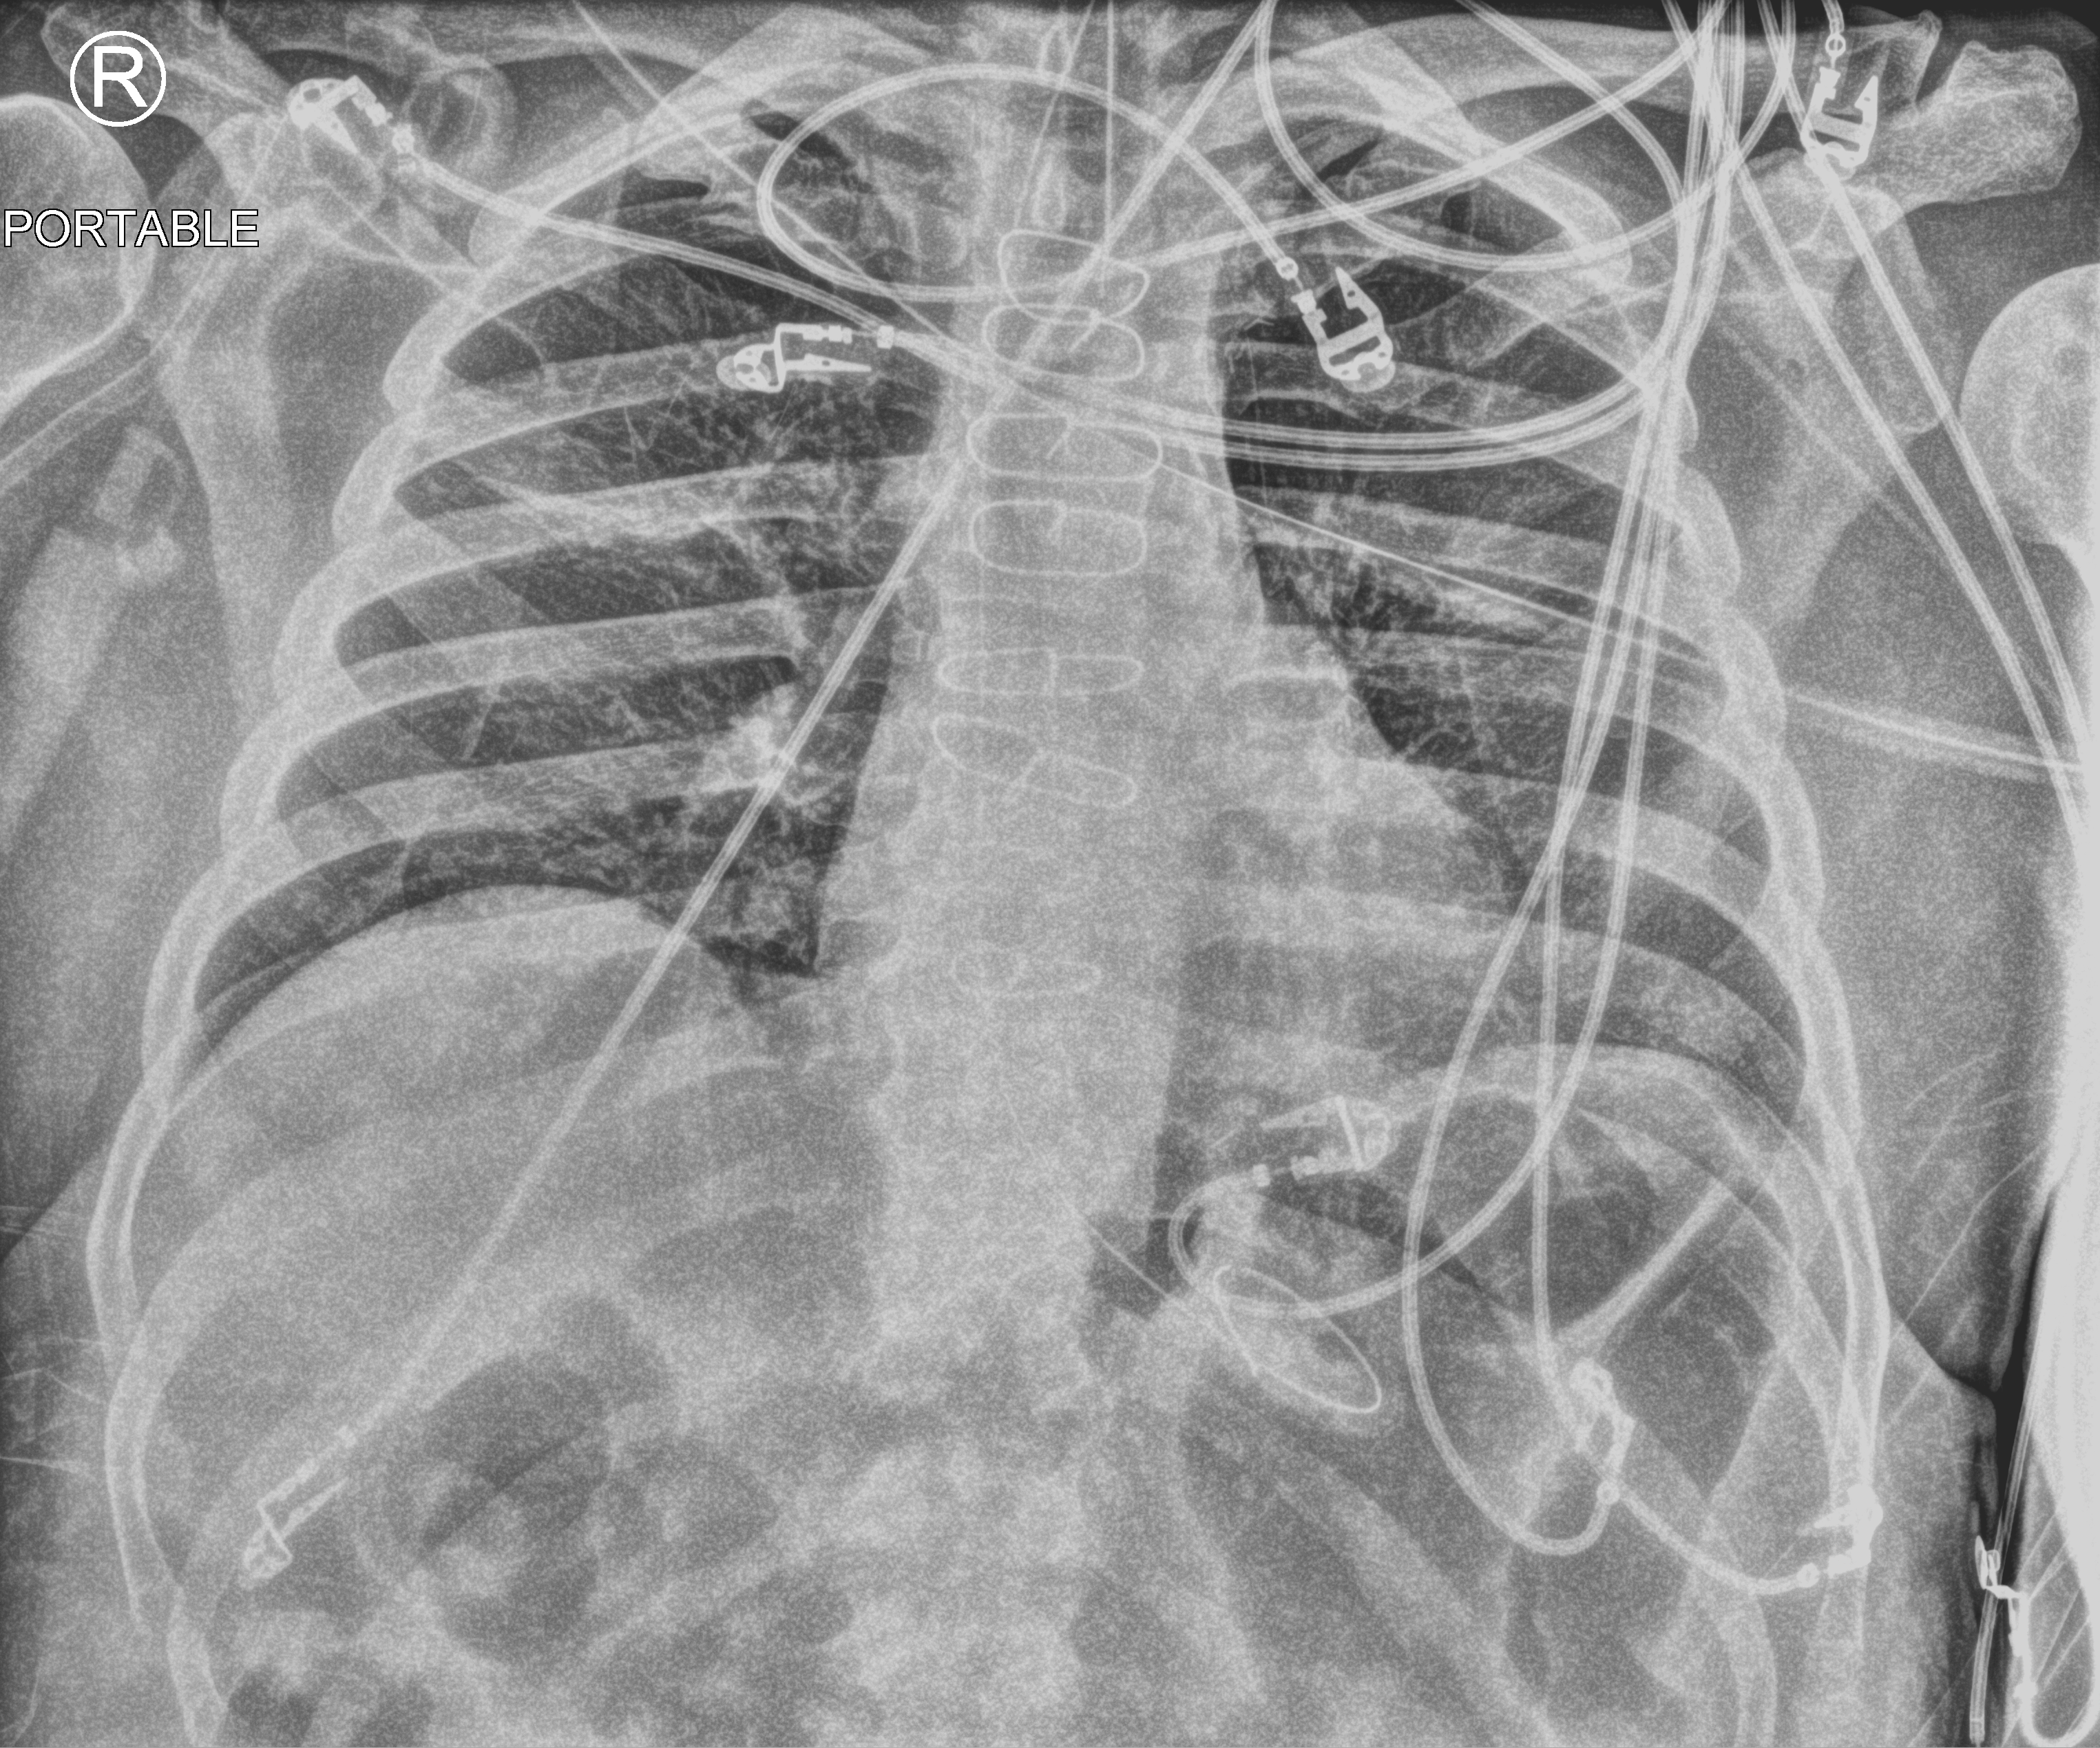
Chest X-ray (portable). Patient hospitalised with COVID-19; male, aged 60–74 years.
Admission-level facts for this patient (not findings on this image; timing relative to this image not recorded):
- length of hospital stay: 44 days
- COPD (admission record): no